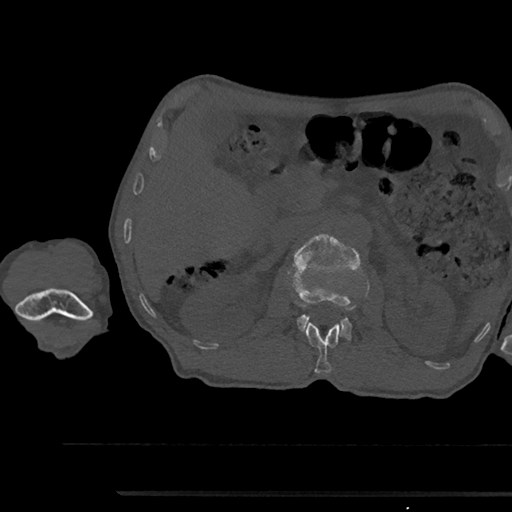
CT including the spine, one axial slice; slice 606 of 797 in the series (ordered by position); 120 kVp; bone window (W 1800 / L 400 HU); 0.5 mm slice thickness; 512 × 512 image matrix, field of view 367 × 367 mm. Patient: male, 79 years. From the clinical record (not read from this slice): primary cancer: prostate.
Structures marked on this image (semi-automatically segmented with operator editing):
- L1 vertebra: box from (x=305, y=322) to (x=340, y=374) px
- L2 vertebra: (x=292, y=234)–(x=362, y=340)